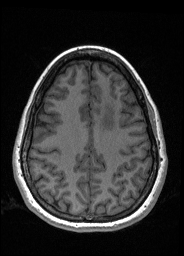
Pre-operative brain MRI before brain-tumour surgery, one axial slice; position 63 of 176 along the scan axis; T1-weighted post-contrast; 1 mm slice thickness; 184 × 256 image matrix, field of view 180 × 250 mm. Case-level facts recorded for this patient, not image findings: histopathology: Oligodendroglioma; WHO grade: 2; IDH mutation: yes; tumour location: Left Frontal.
Annotated regions visible in this slice (outlined manually by an expert reader):
- tumour: bounding box (x1, y1, x2, y2) in pixels: (100, 99, 116, 130)